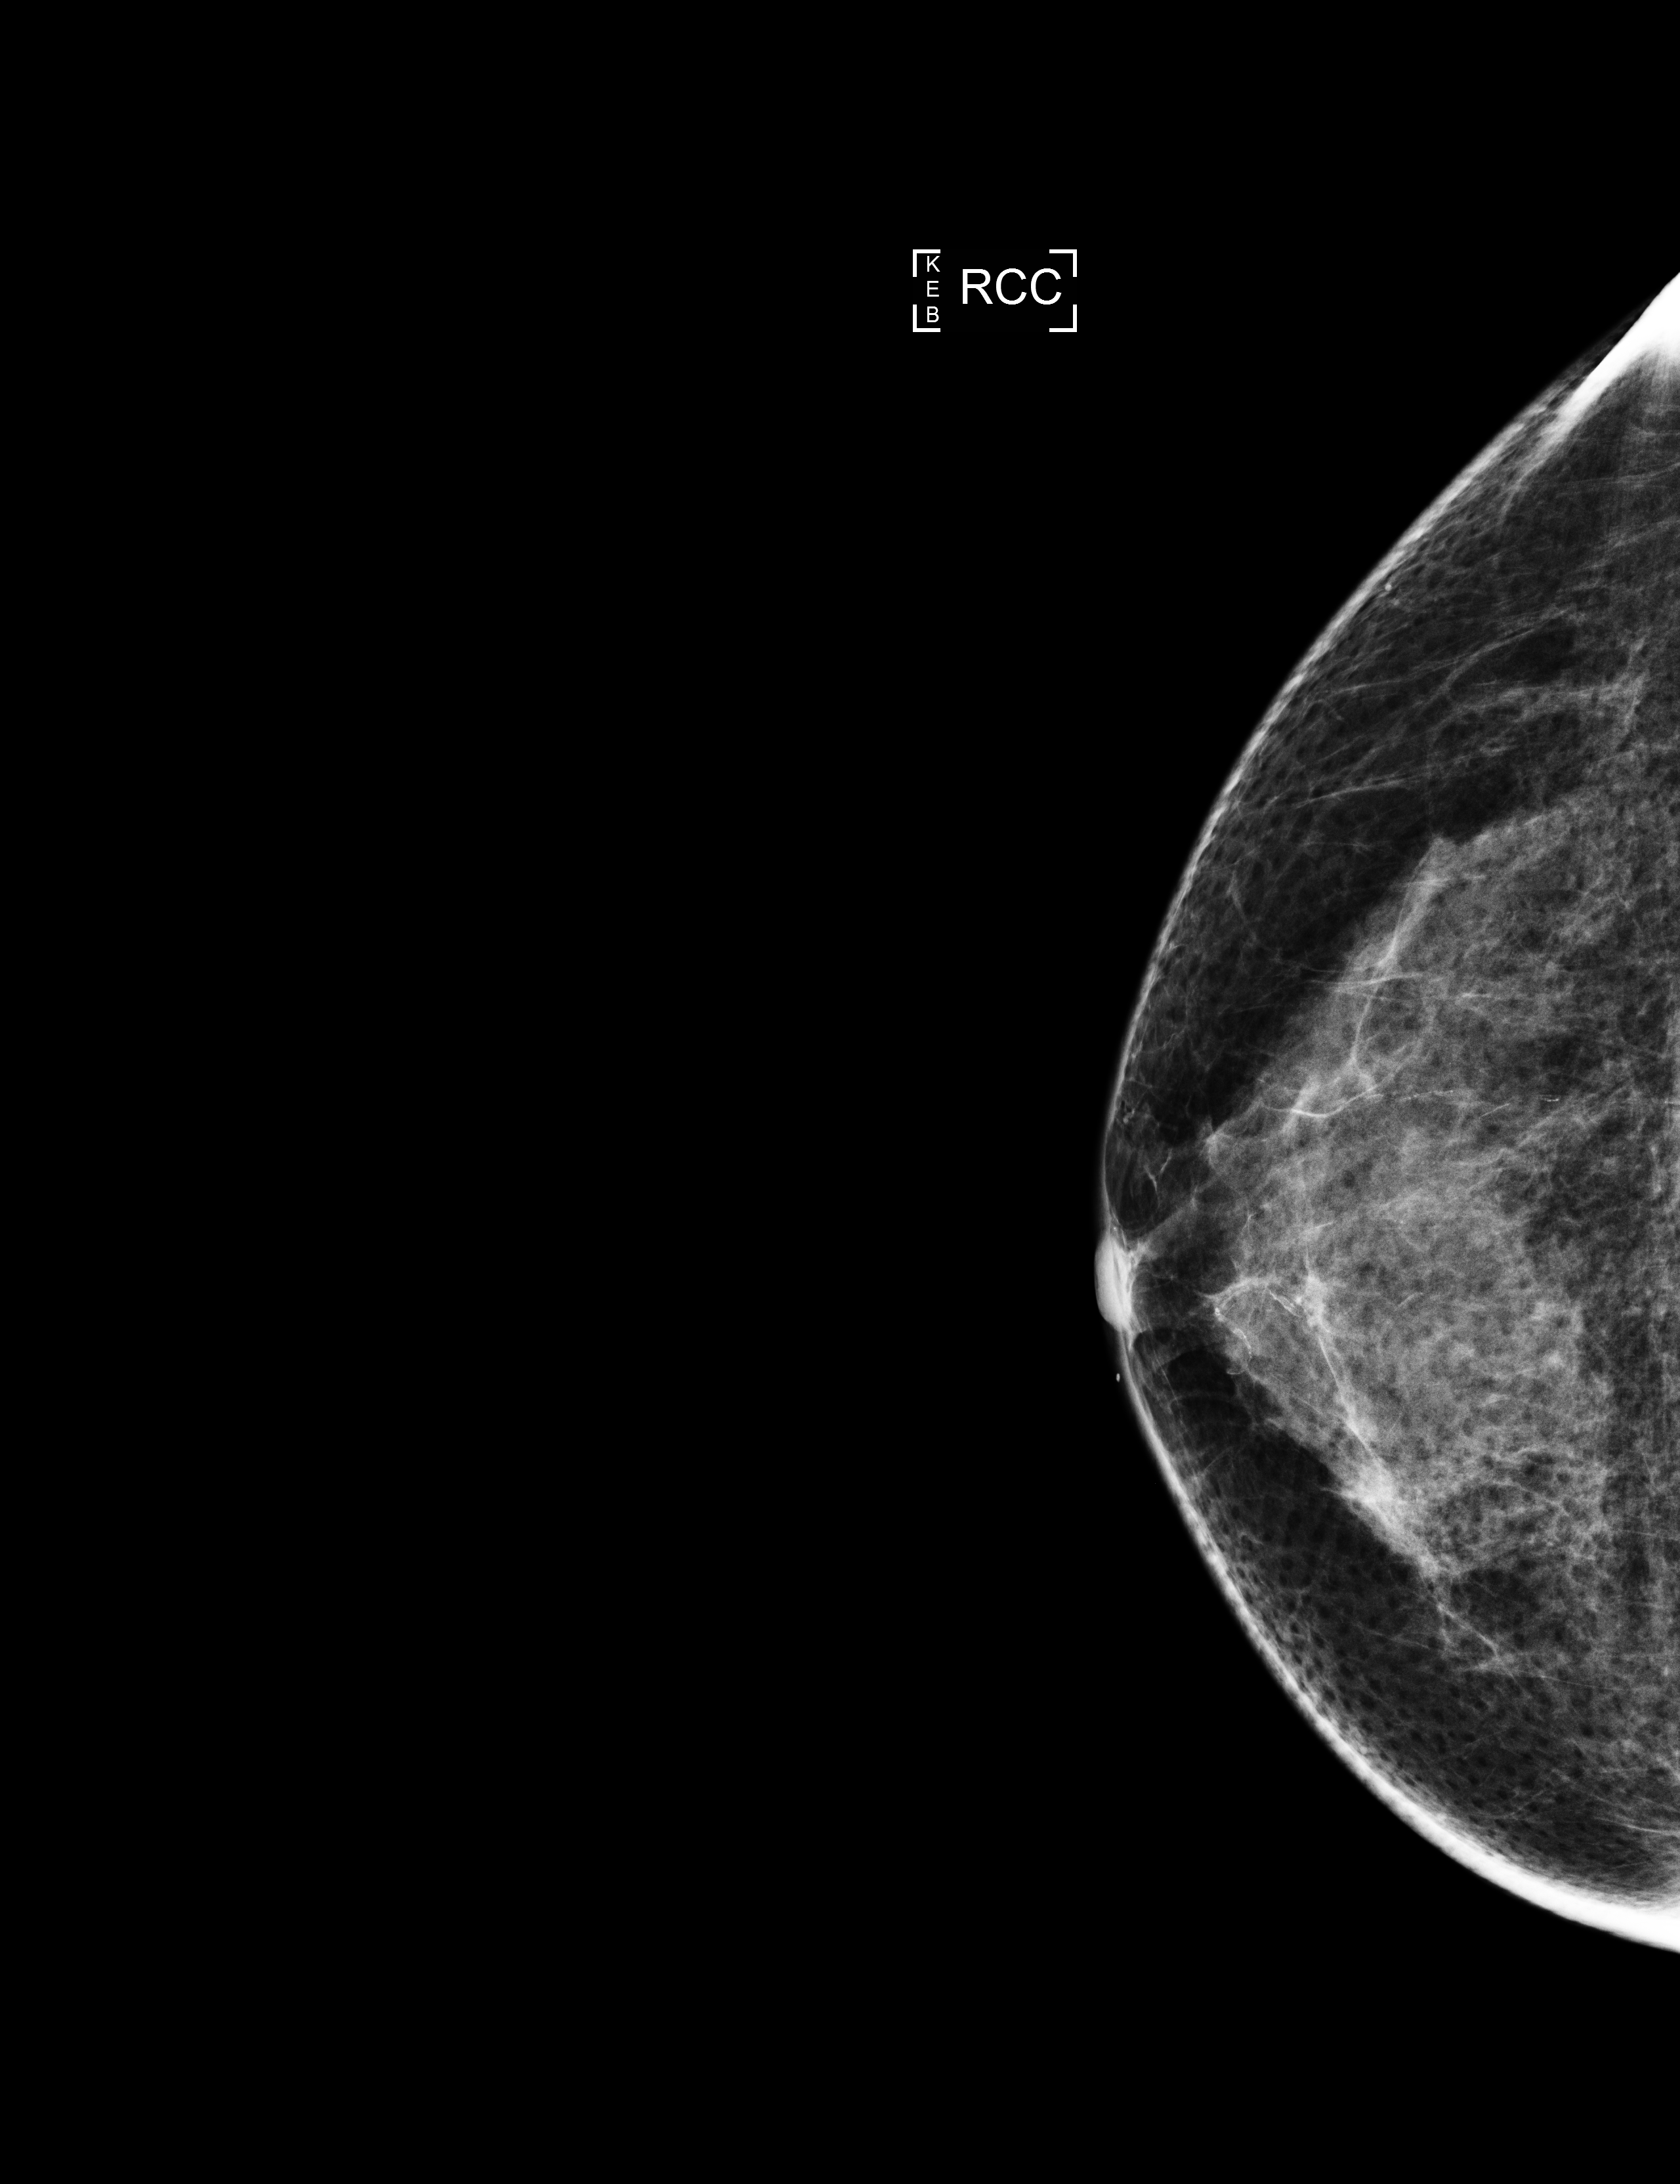
Screening examination. Patient: female, 64 years.
Image type: full-field digital mammogram. Breast: right. Projection: cranio-caudal projection. Breast density at the screening exam (both breasts): extremely dense (BI-RADS density category d). Final BI-RADS category for the screening round (tomosynthesis exam, both breasts): category 1. Recall: no recall after this screen.